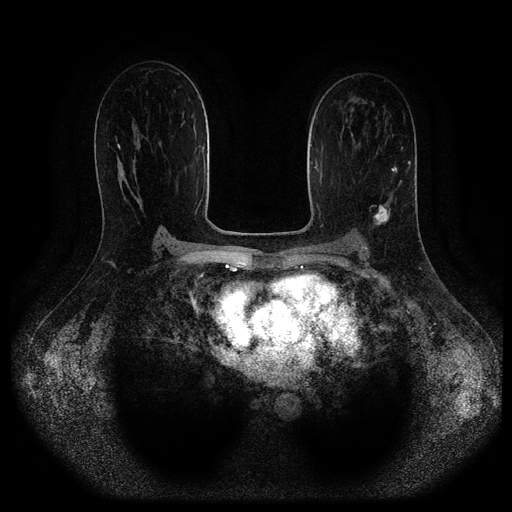
Breast MRI (dynamic contrast-enhanced, multi-phase), one axial slice; dynamic contrast-enhanced series, time point 2 of 5 at this slice position (early post-contrast); 1.5 T; TE 2.6 ms, TR 5.3 ms; 2 mm slice thickness; 512 × 512 image matrix, field of view 370 × 370 mm. Patient: female, 45 years.
Annotated regions visible in this slice (semi-automatic segmentation, software-assisted and operator-edited):
- breast lesion (labelled 'tumour' in the annotation; benign lesions carry a separate 'benign' label): bounding box <373,203,391,226> (left, top, right, bottom; pixels)